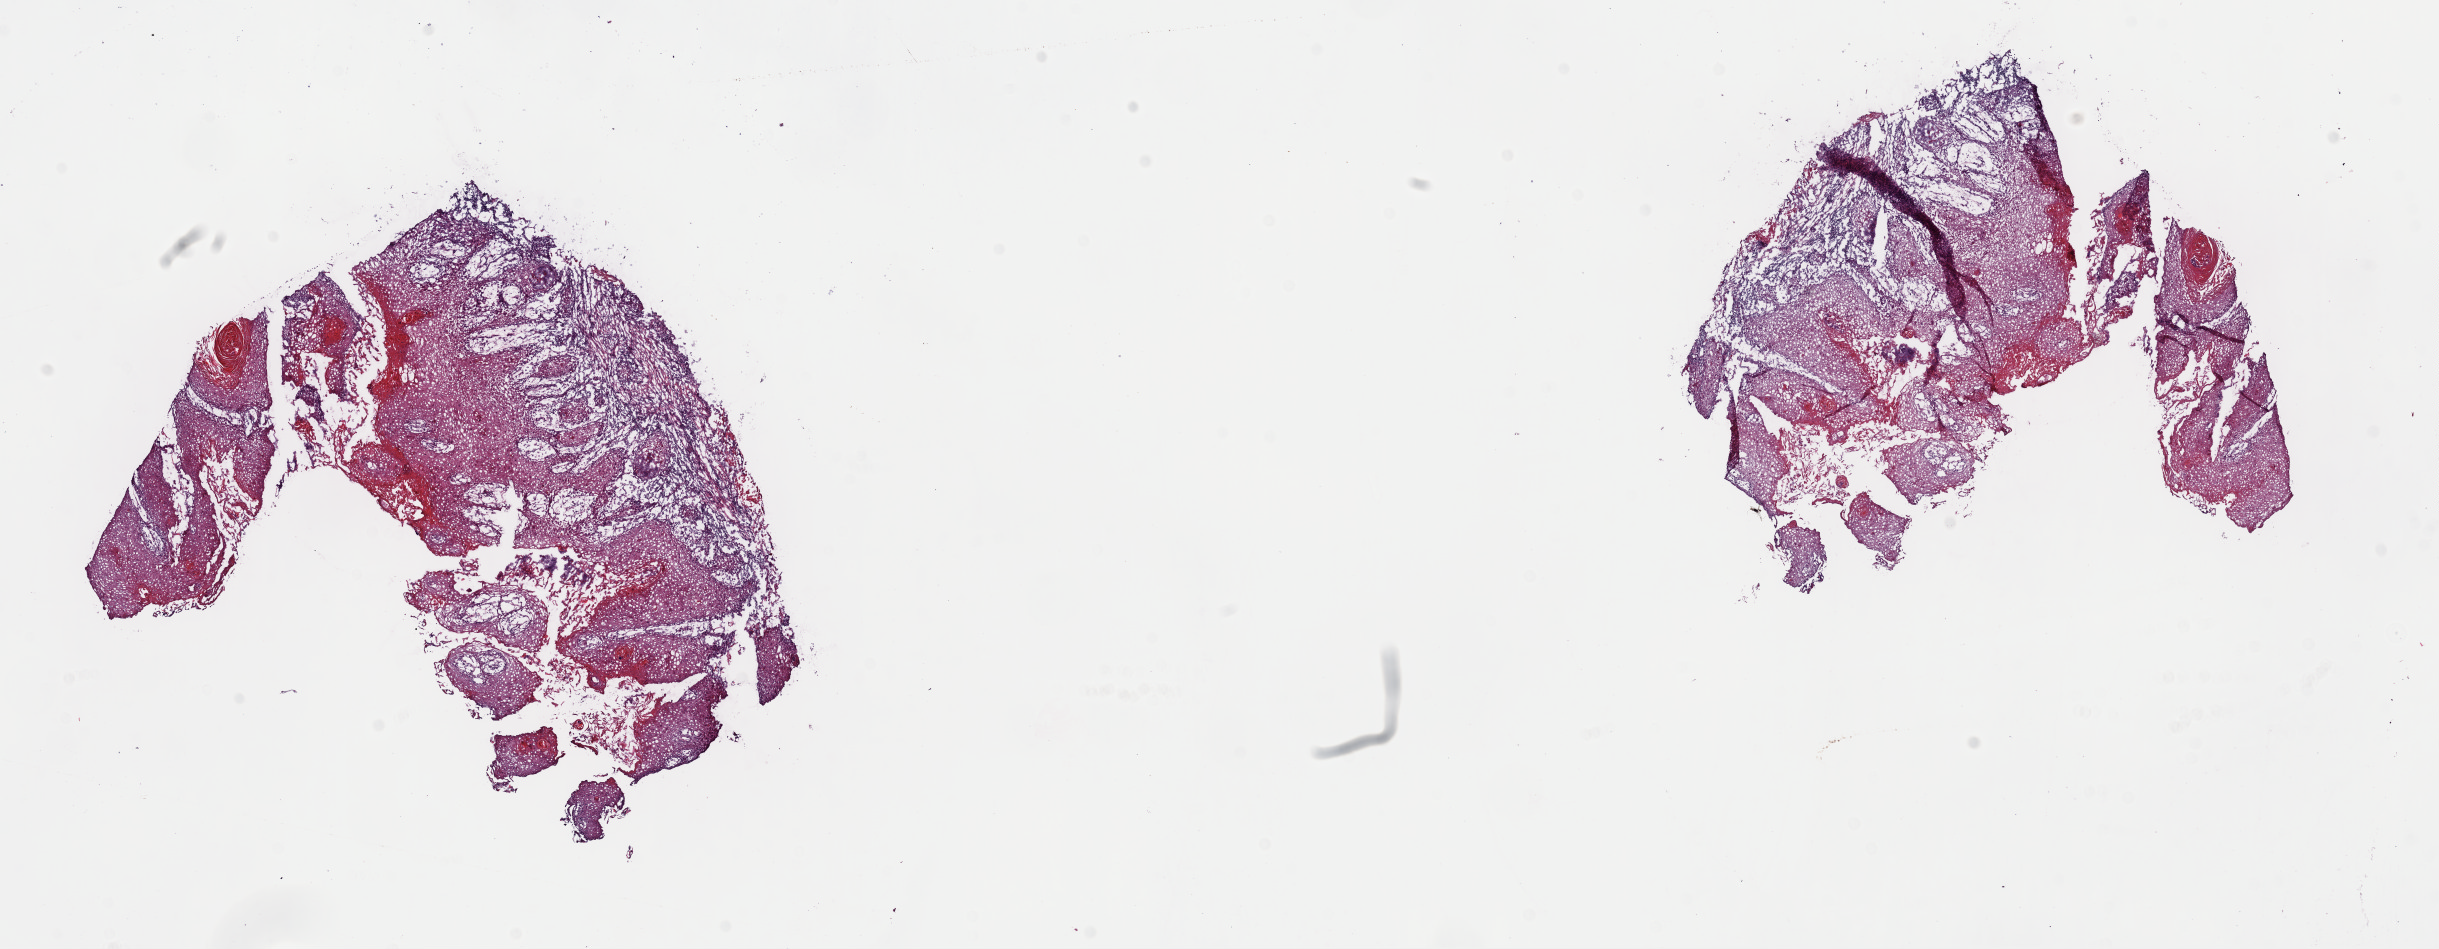
Digitized H&E tissue section (whole slide) — shown as a low-resolution overview of the whole scanned area (about 19.3 x 7.5 mm). Frozen section from the top of the tissue portion. Primary tumour sample from the head and neck. Male patient; age at initial diagnosis 57 years.
Diagnosis: Squamous cell carcinoma, NOS.